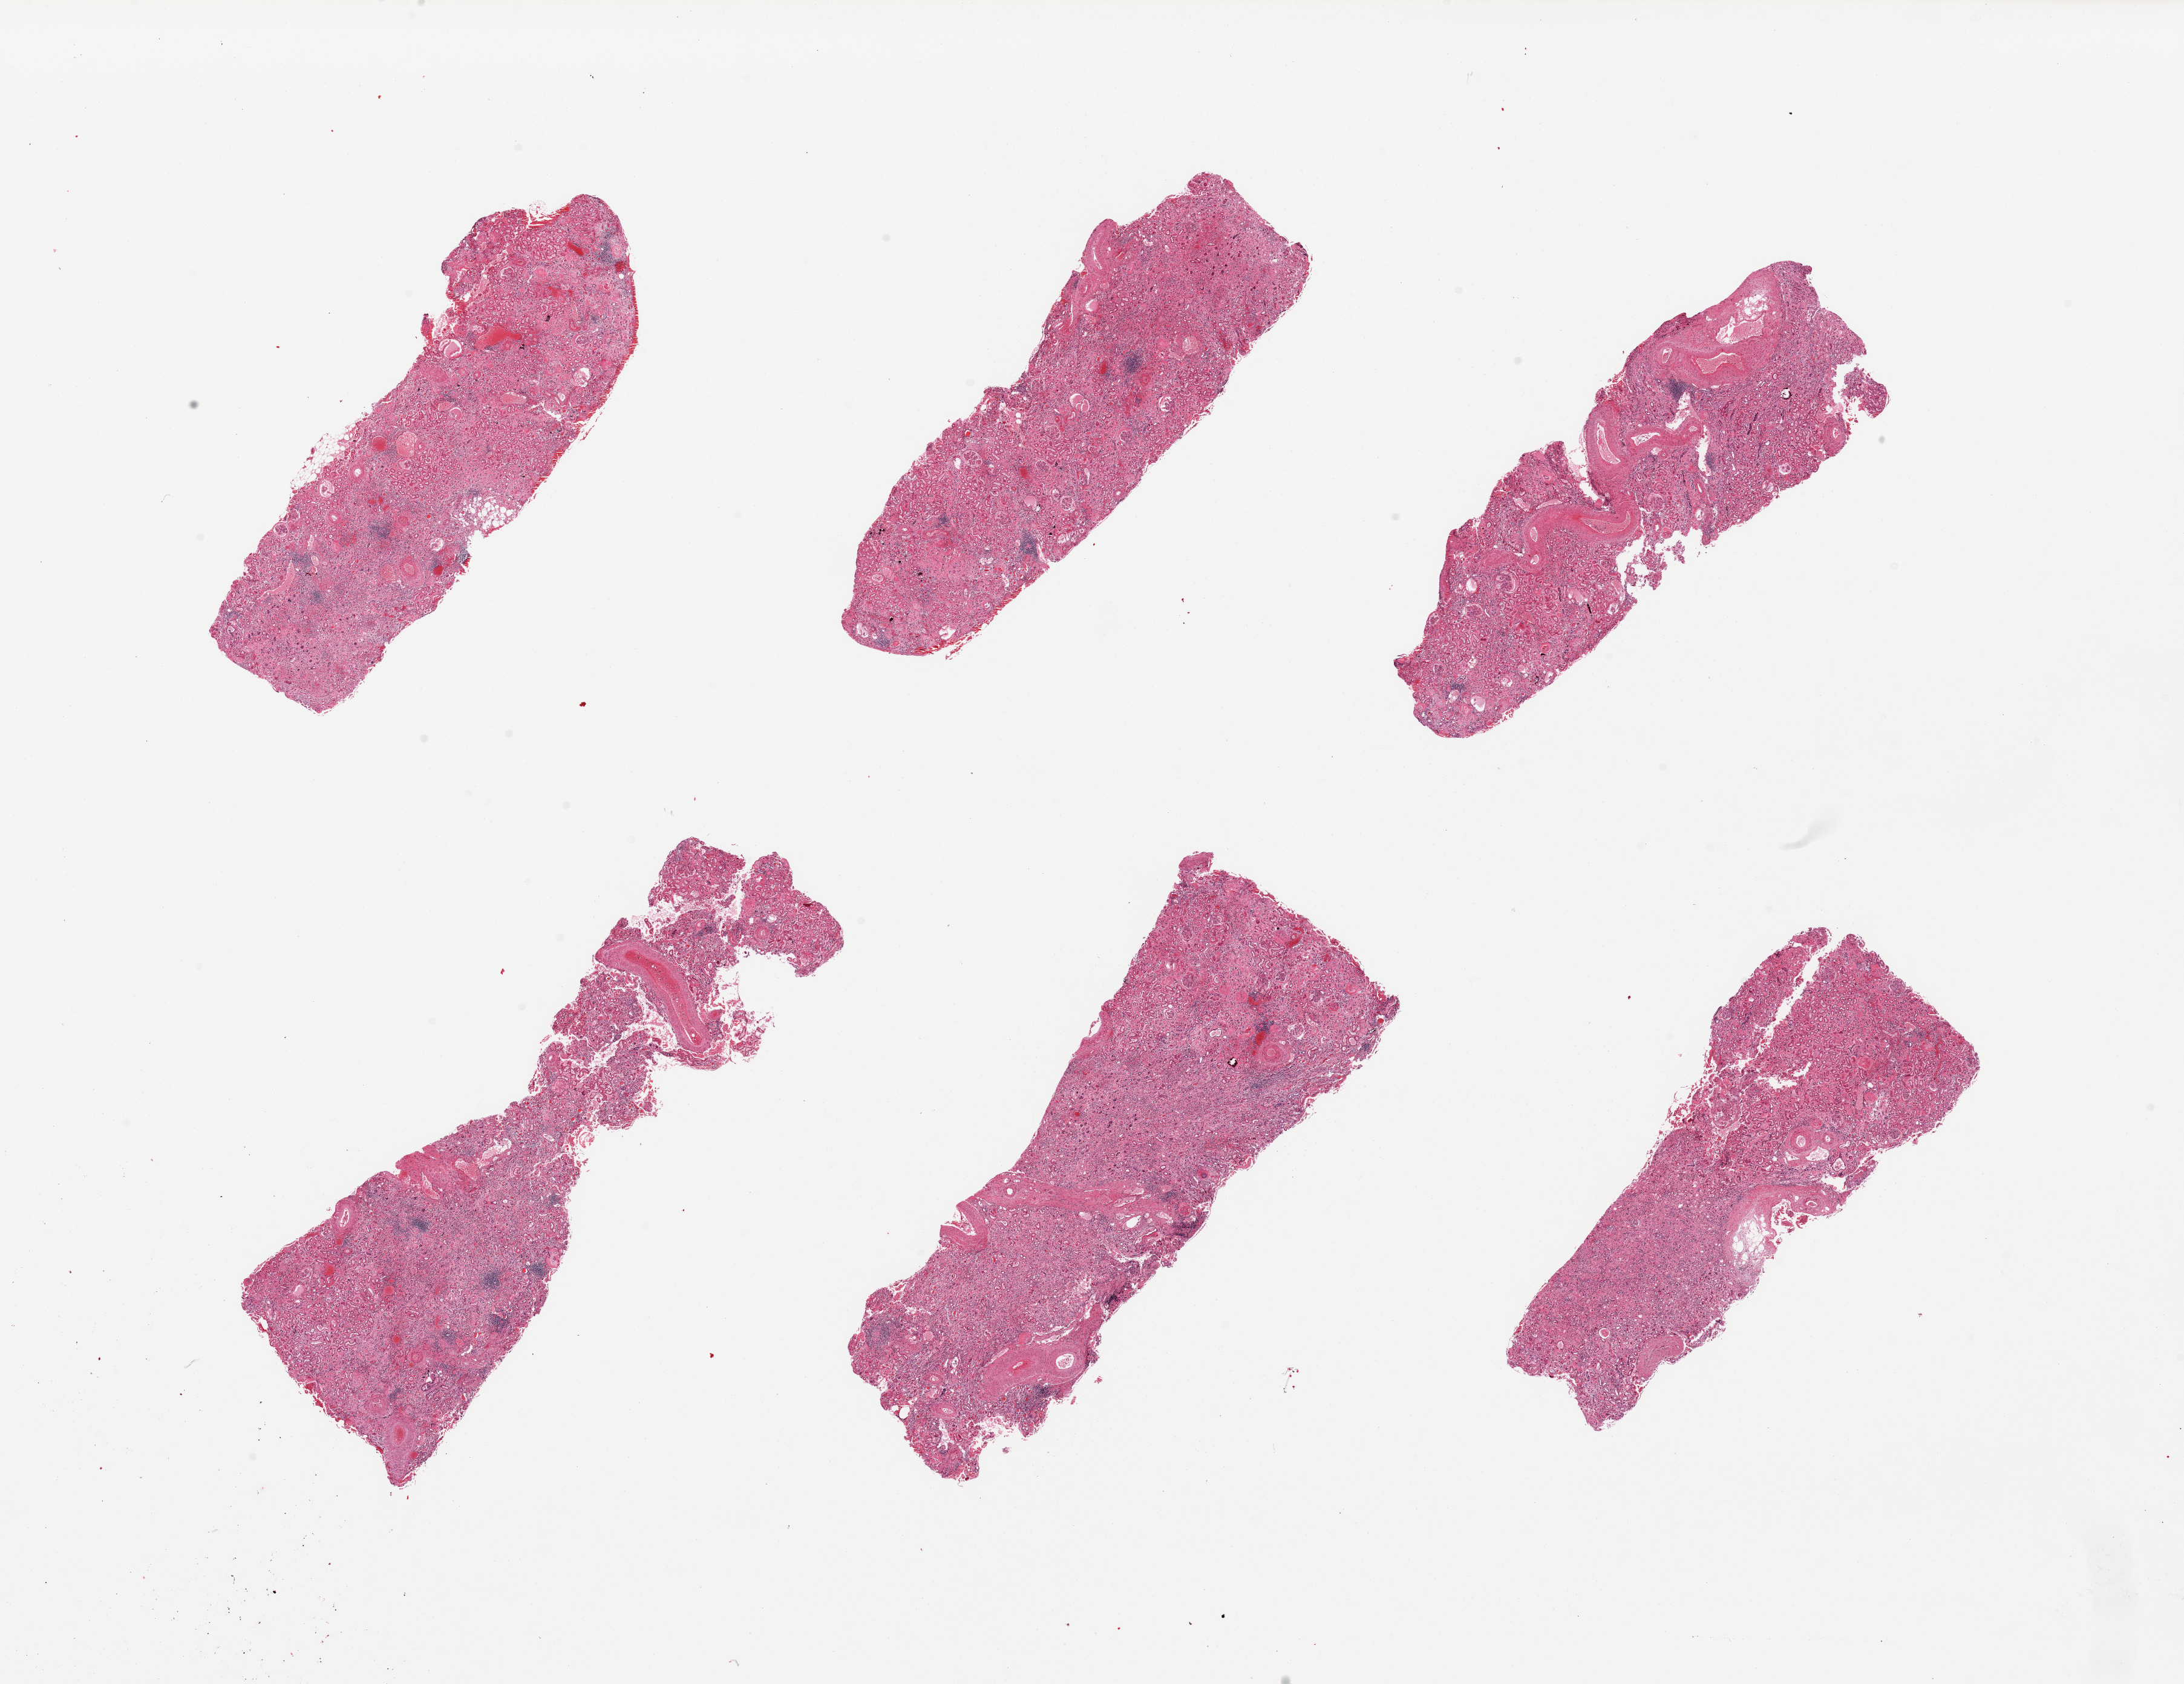
Haematoxylin and eosin whole-slide image, brightfield, whole scanned area (about 28.5 x 22.0 mm, from a 20x scan) shown as a low-resolution overview. PAXgene-fixed paraffin-embedded (PFPE) section. Target tissue: renal cortex. Tissue donor sample. Female donor.
Review note (as recorded): 6 pieces; severe glomerular and vascular sclerosis; both cortex and medulla represented.